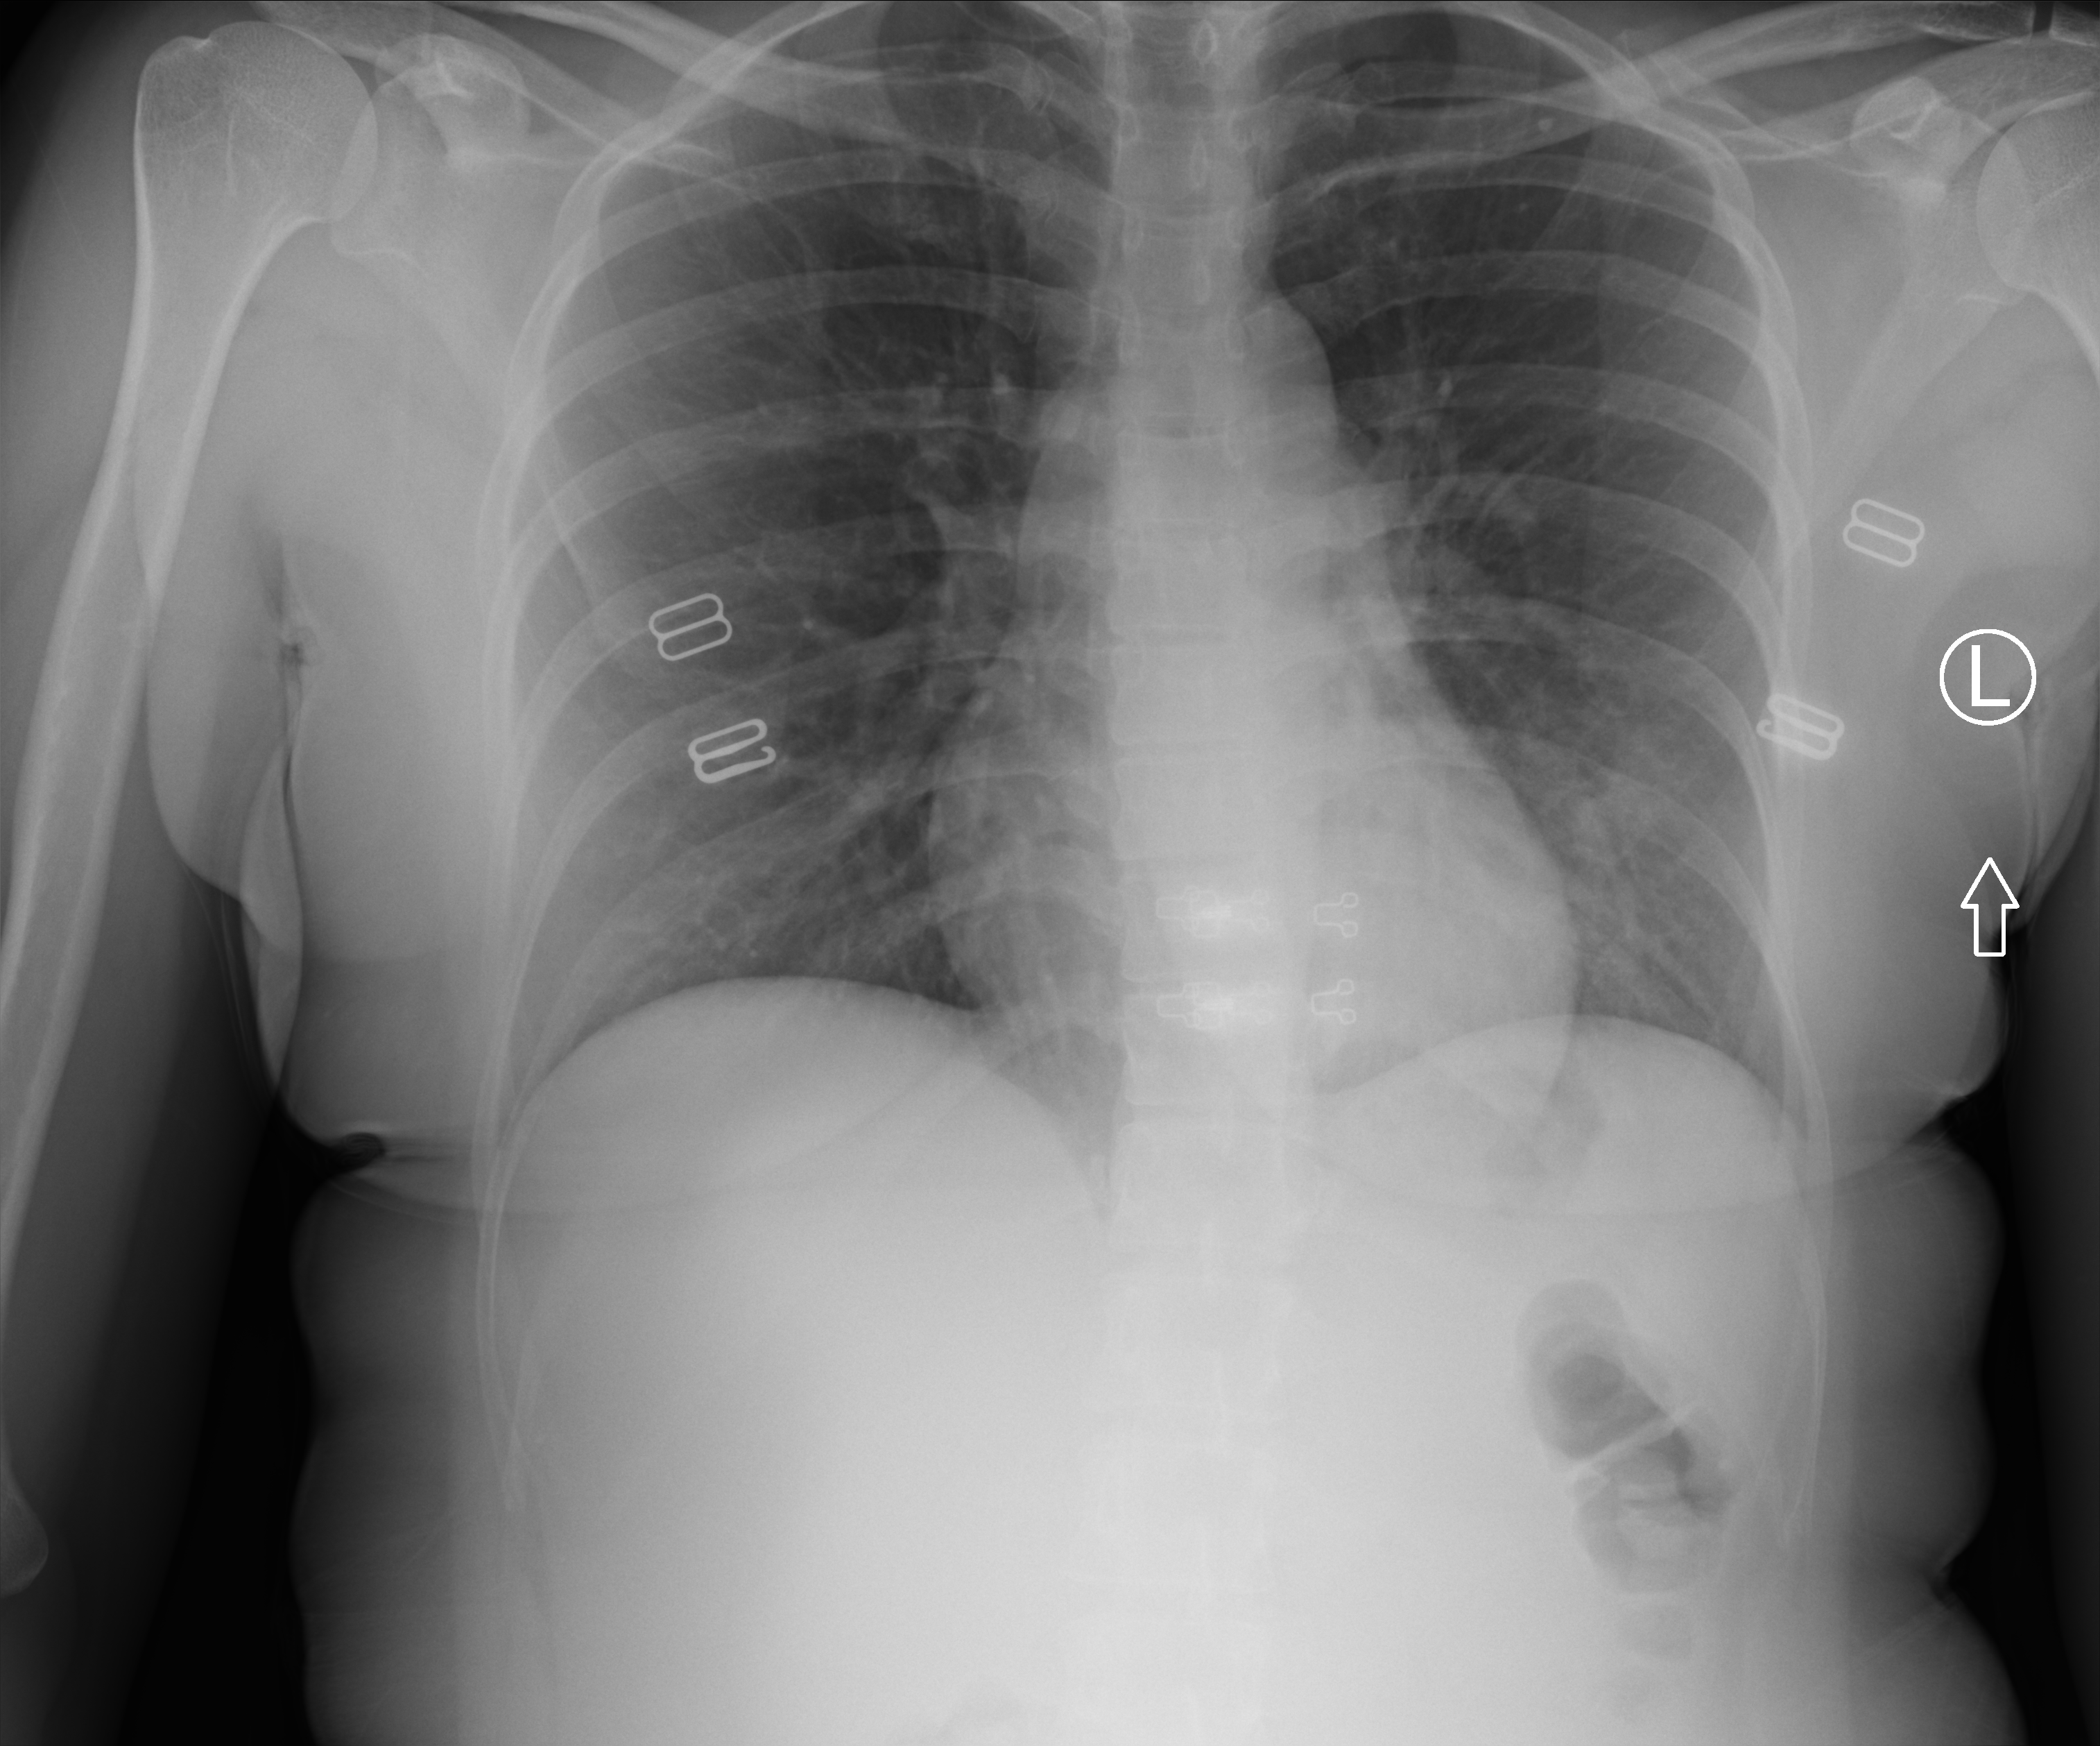
Bedside chest radiograph (computed radiography); anteroposterior (AP) projection. Patient hospitalised with COVID-19; female, aged 18–59 years.
Admission-level facts for this patient (not findings on this image; timing relative to this image not recorded):
- mechanically ventilated during this hospital stay: no
- admitted to intensive care during this hospital stay: no